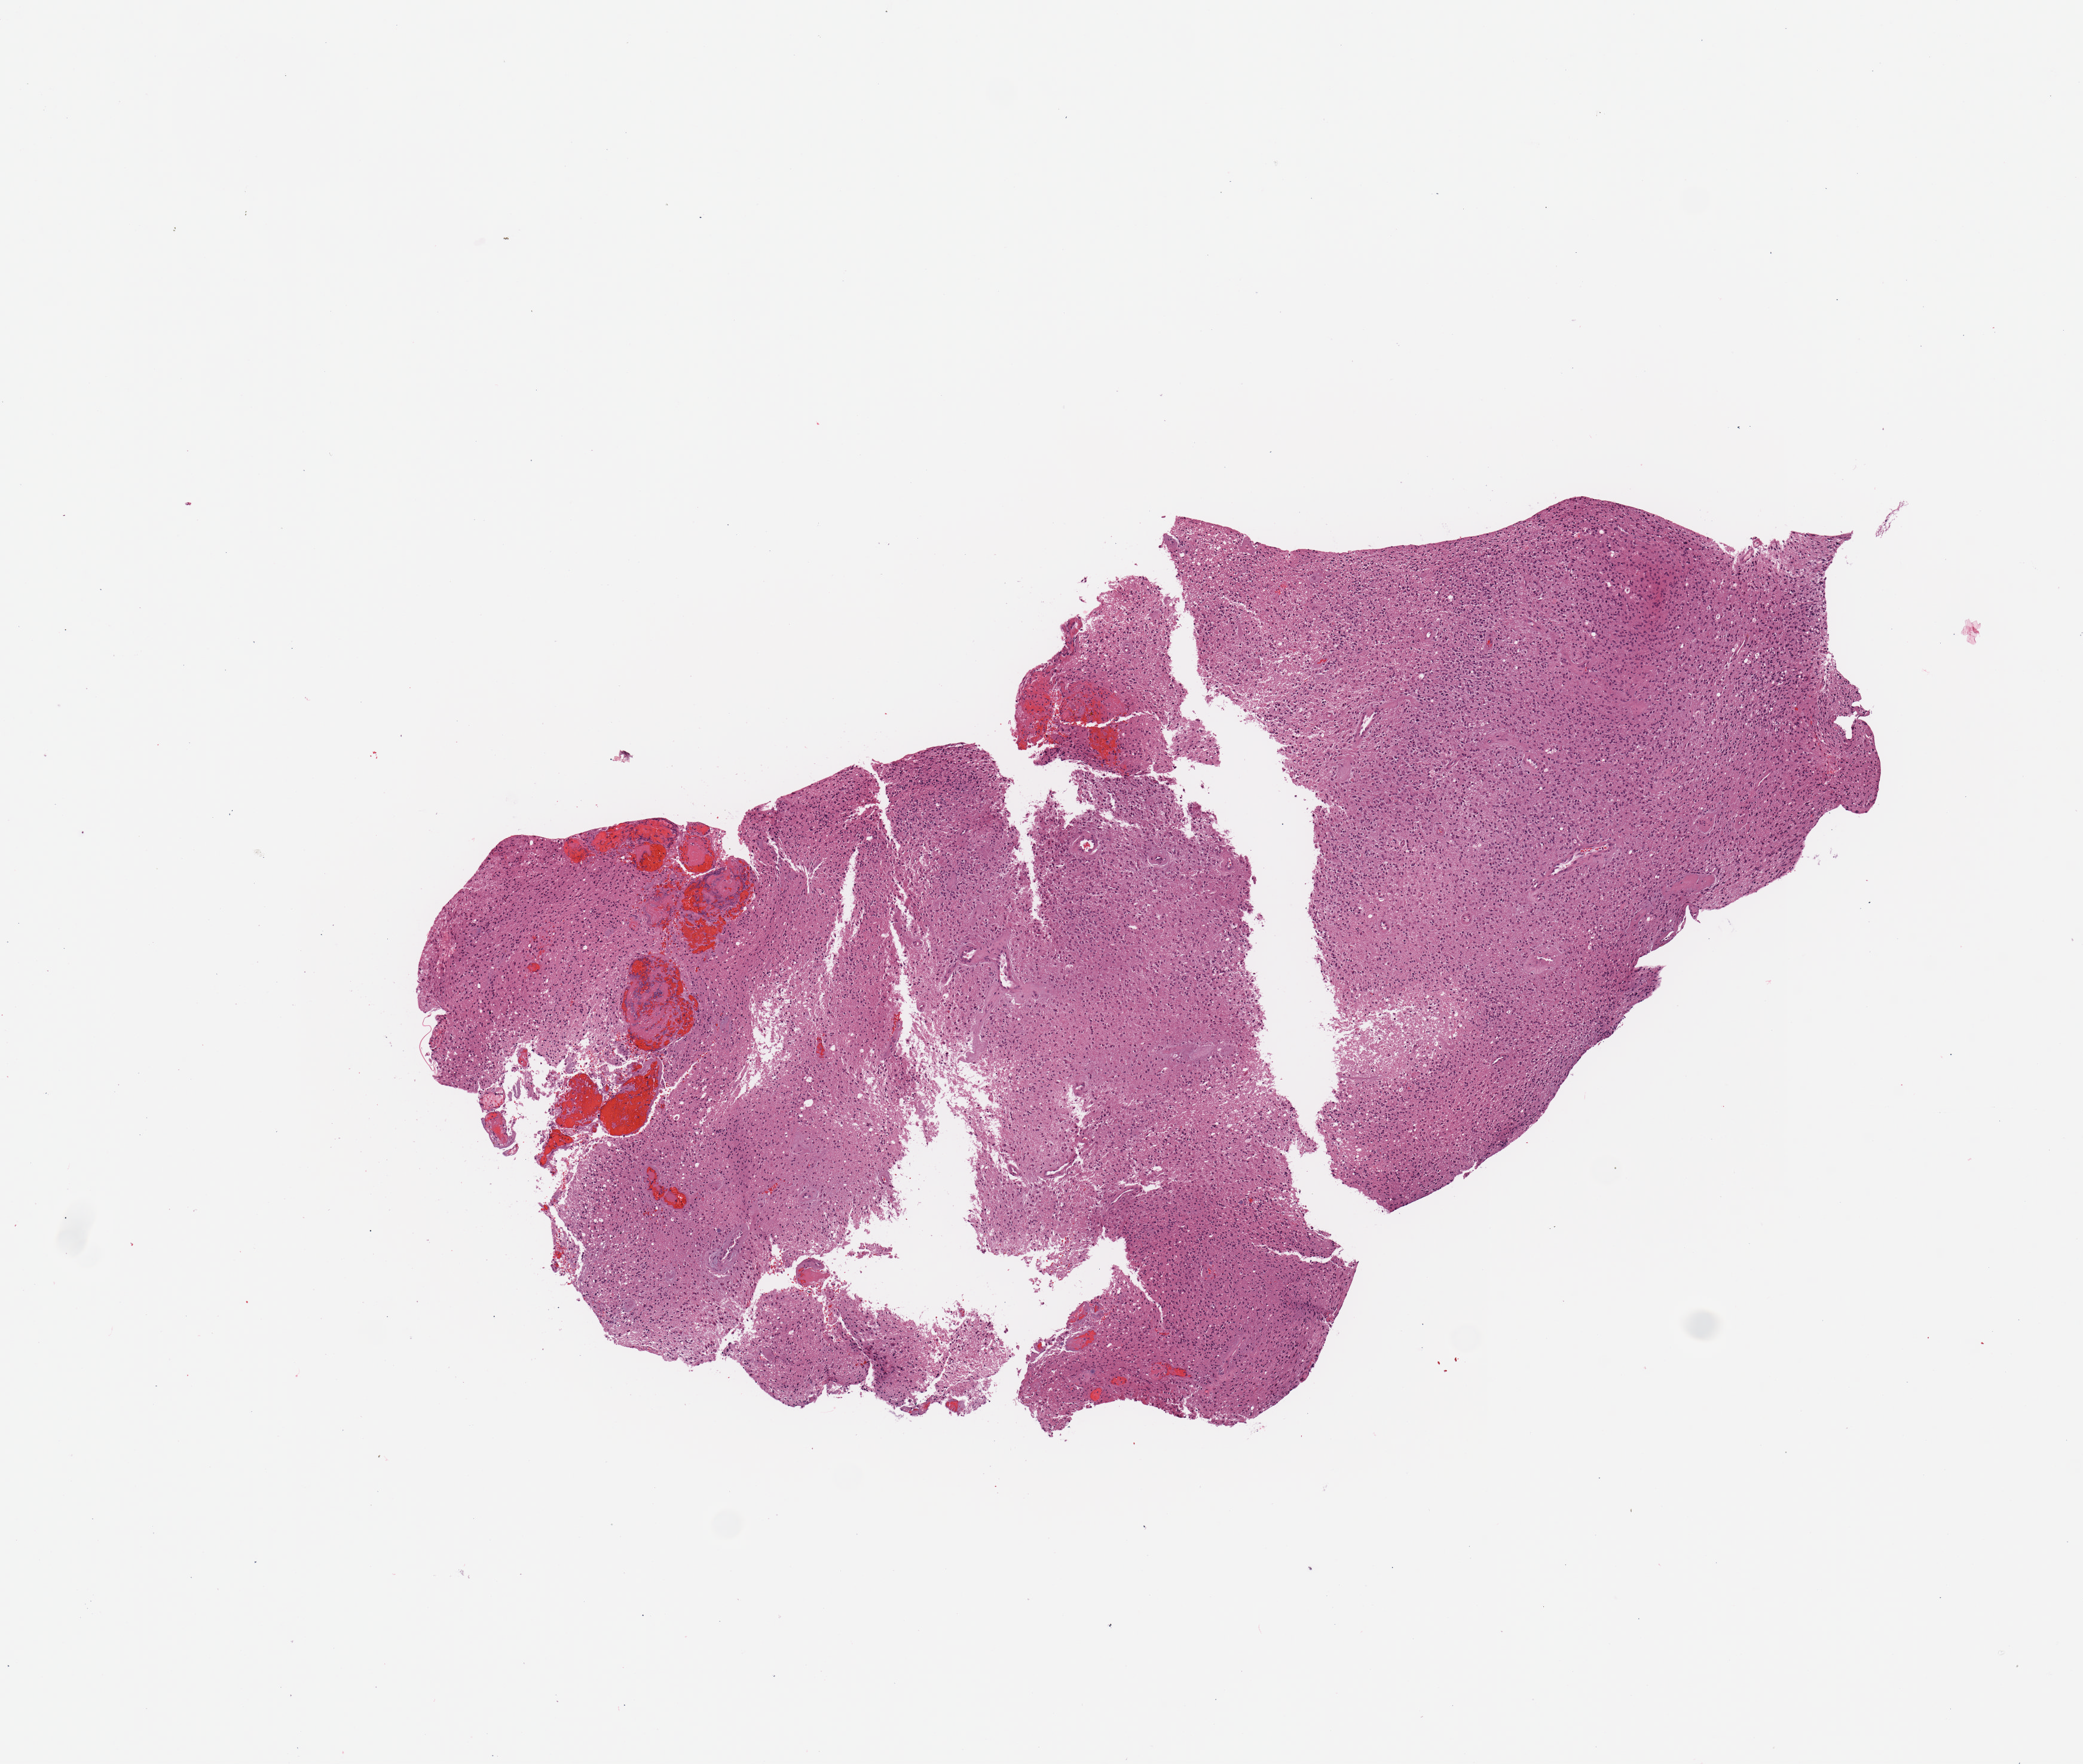
Whole-slide histology image, H&E-stained — a low-resolution overview of the entire scanned area, about 6.9 x 5.8 mm (from a 20x scan); tumour tissue sample, sampled site: brain. Patient: female, age 61 years. Composition of this section per pathologist review: tumour nuclei 85%, necrosis 5%.
• primary tumour site (as recorded): parietal lobe
• histologic diagnosis: Glioblastoma